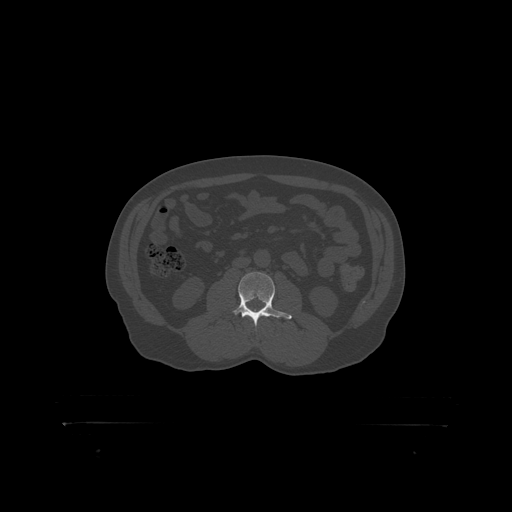
CT including the spine, one axial slice. Position 267 of 399 along the scan axis. Reconstruction kernel STANDARD. Bone window (W 1800 / L 400 HU). 1.25 mm slice thickness. 512 × 512 image matrix, field of view 650 × 650 mm. Male patient, age 46 years. Case-level facts recorded for this patient, not image findings: primary cancer: skin.
Outlined on this slice (semi-automatically segmented with operator editing):
- L3 vertebra: bounding box [x1, y1, x2, y2] px = [233, 273, 282, 319]